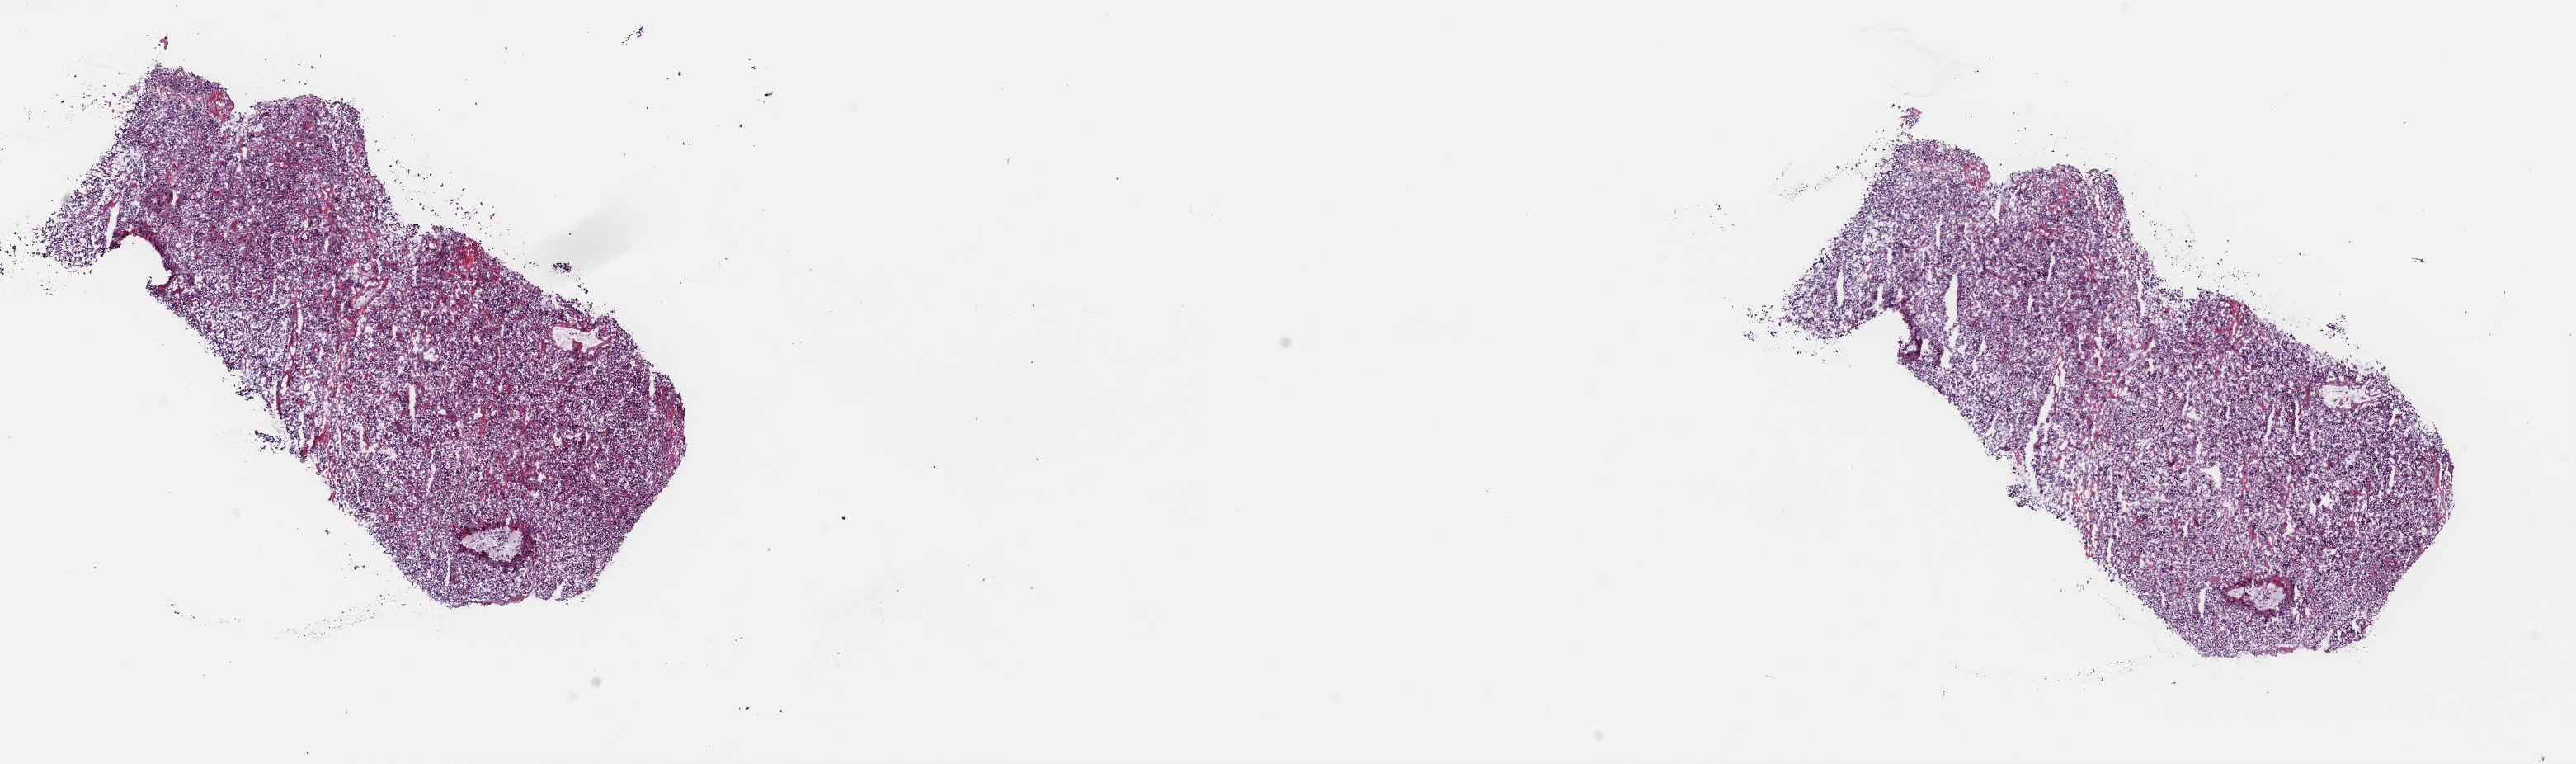
H&E whole-slide image — low-resolution overview of the scanned area, about 24.7 x 7.3 mm (from a 40x scan). Frozen section from the top of the tissue portion. Primary tumour sample from the adrenal gland. Male, age 31 years at initial diagnosis. Pathologist review of this section (percent, as recorded): tumour cells 100%, tumour nuclei 80%, normal cells 0%, stromal cells 0%, necrosis 0%. Inflammatory infiltration, as recorded: lymphocyte infiltration 1%, monocyte infiltration 0%, neutrophil infiltration 0%.
Histologic diagnosis: Pheochromocytoma, NOS.